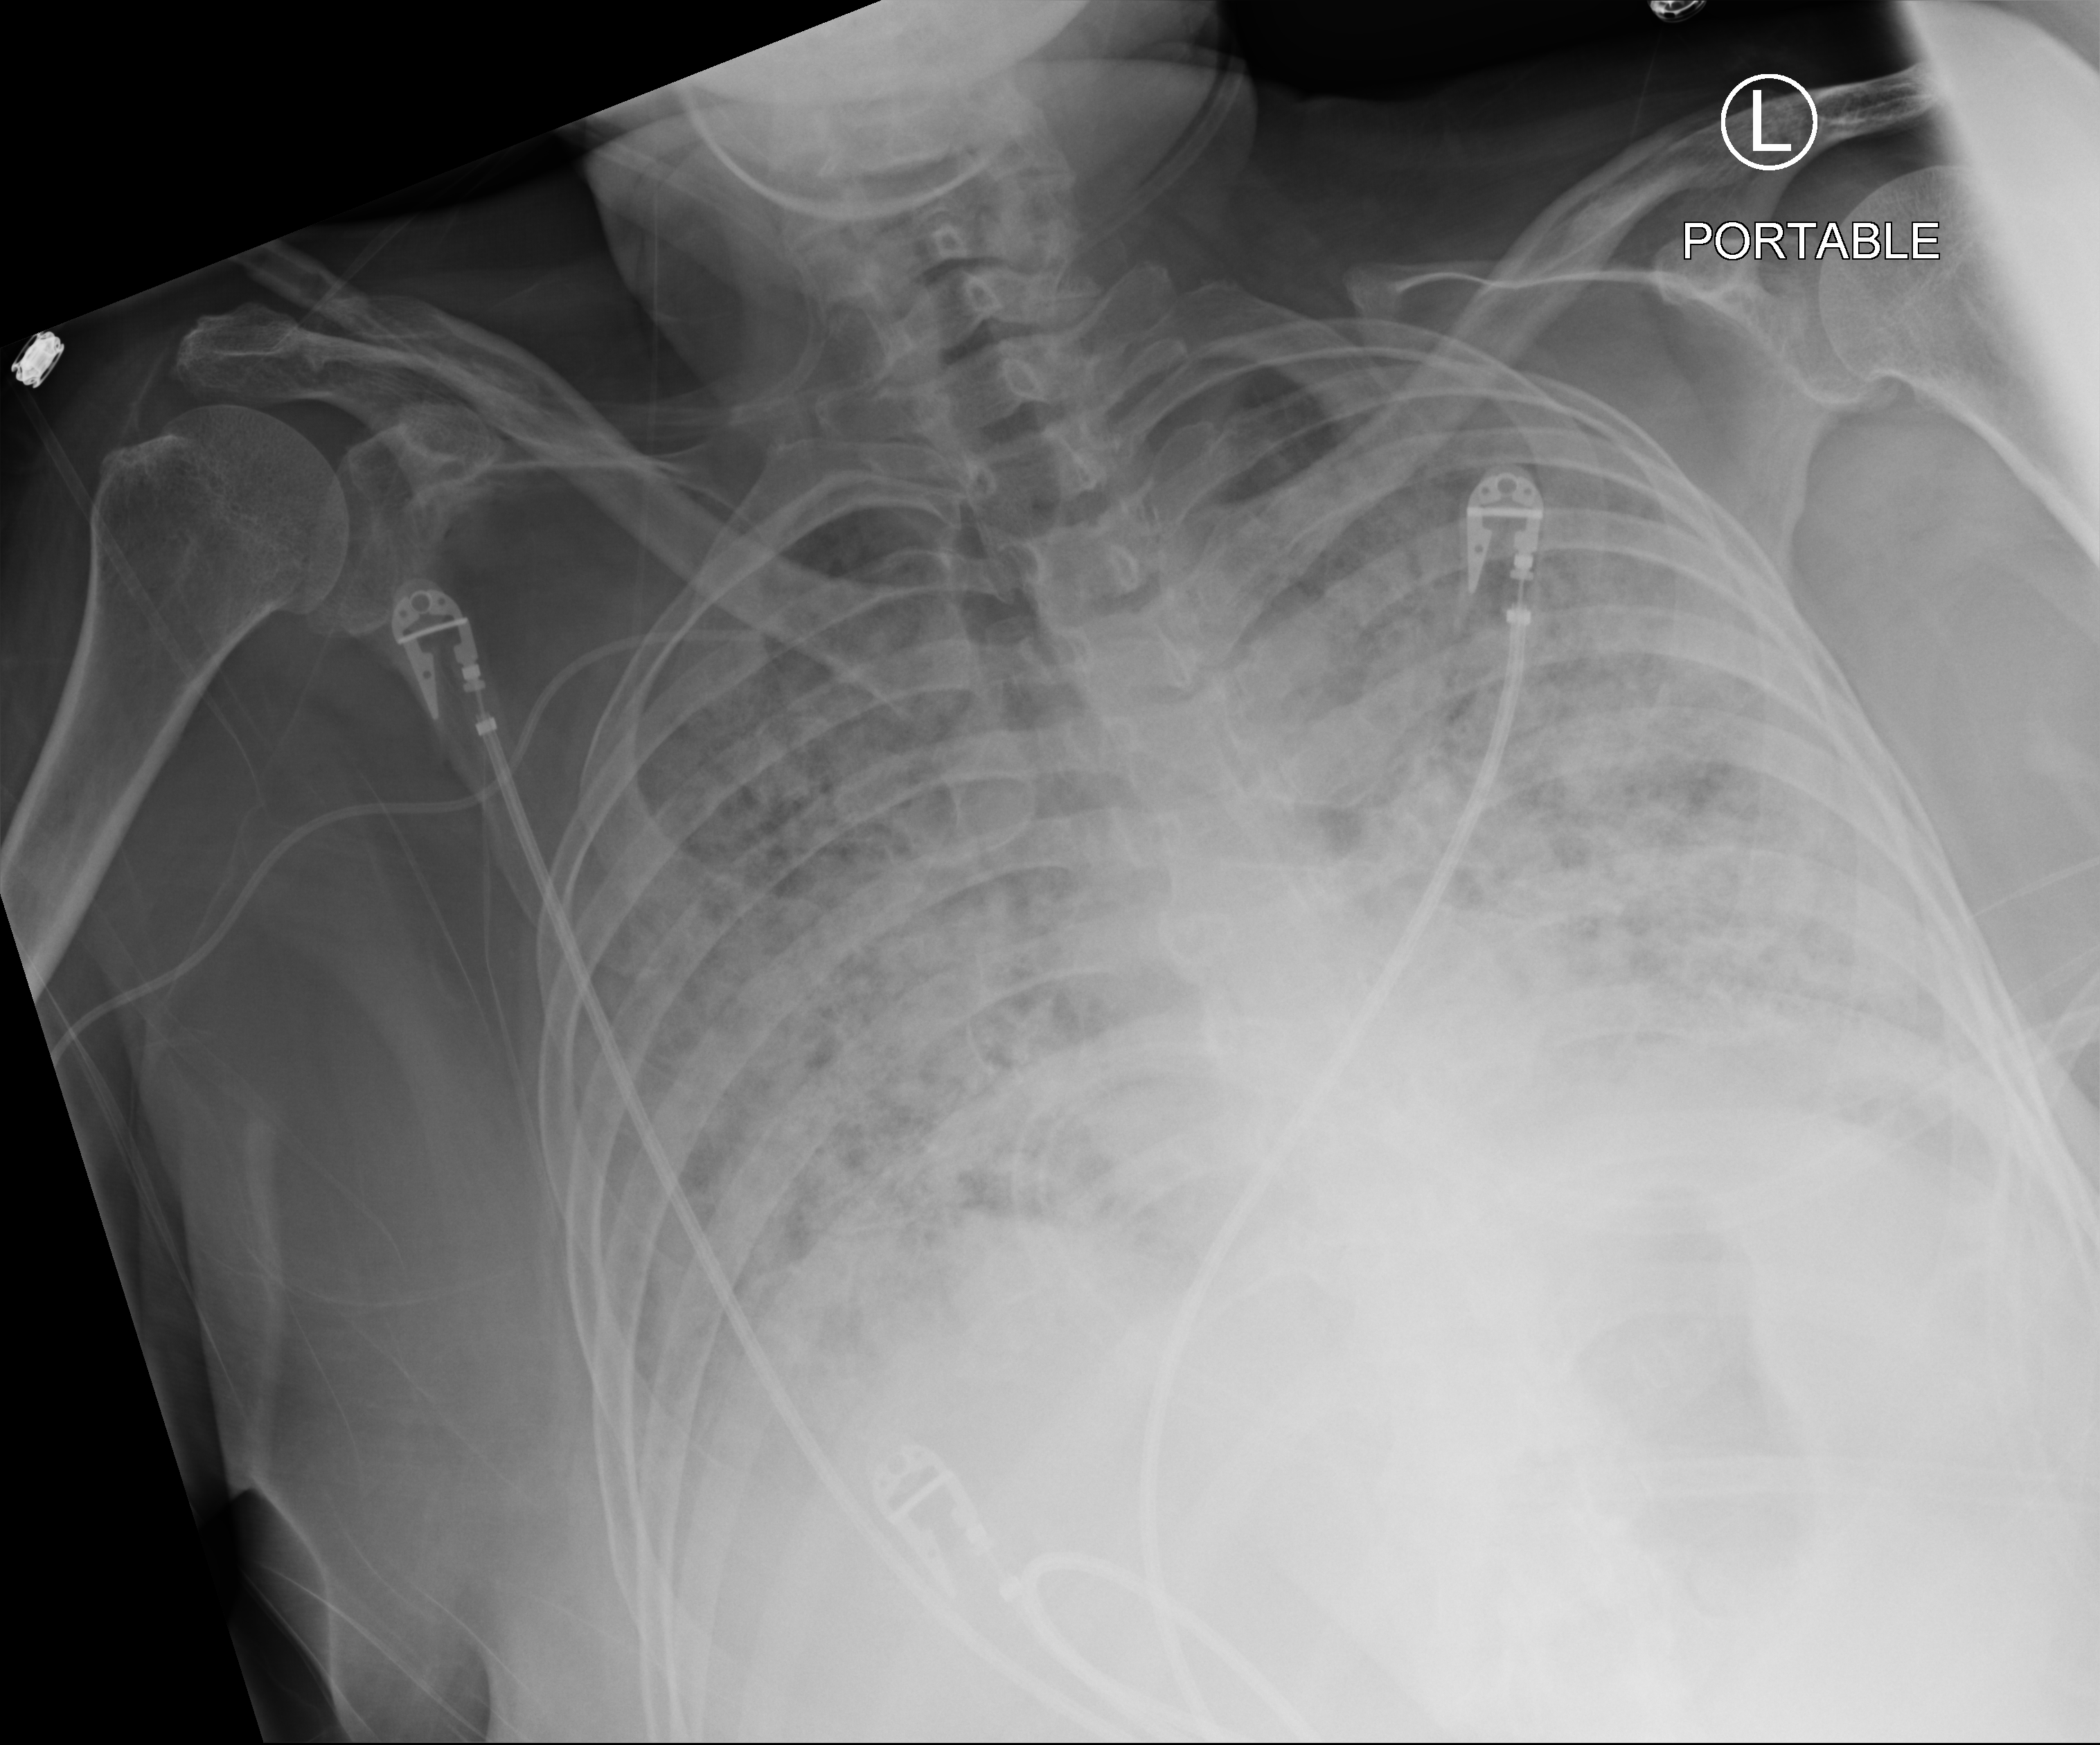
Portable chest radiograph, anteroposterior (AP) projection. Patient hospitalised with COVID-19; female, aged 75–90 years.
From the hospital-stay record, not from the radiograph (when in the stay this image was taken is not recorded):
- admitted to intensive care during this hospital stay: yes